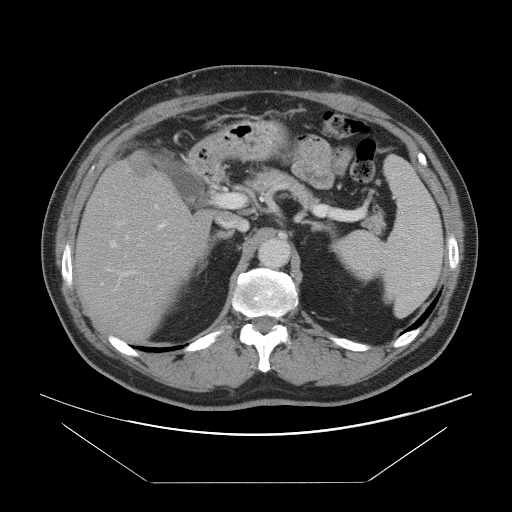
Contrast-enhanced abdominal CT, one axial slice; position 54 of 97 along the scan axis; intravenous contrast given; soft-tissue window (W 400 / L 40 HU); 5 mm slice thickness; 512 × 512 image matrix, field of view 442 × 442 mm. Male patient, age 62 years. Case-level facts recorded for this patient, not image findings: diagnosis: colorectal cancer liver metastases, imaged before liver resection; multiple liver metastases: no; largest metastasis: 7 cm; disease in both lobes: yes.
Annotated regions visible in this slice (expert manual segmentation):
- hepatic veins: box from (x=110, y=235) to (x=172, y=258) px
- liver: (x=77, y=154)–(x=212, y=340)
- planned liver remnant (the part of the liver to remain after resection): (x=76, y=176)–(x=211, y=341)
- portal vein (with intrahepatic branches): (x=117, y=194)–(x=228, y=272)
- liver metastasis: (x=128, y=158)–(x=153, y=178)